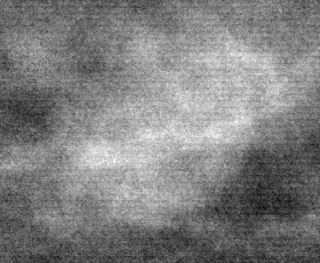
Cropped region of a digitized screen-film mammogram centred on a radiologist-marked abnormality; right breast; CC view; BI-RADS breast density category 1 (scale 1–4).
Finding: mass, shape round, margins circumscribed; BI-RADS assessment category 2; subtlety rating 5 on a 1 (subtle) to 5 (obvious) scale; pathology (as recorded): benign.